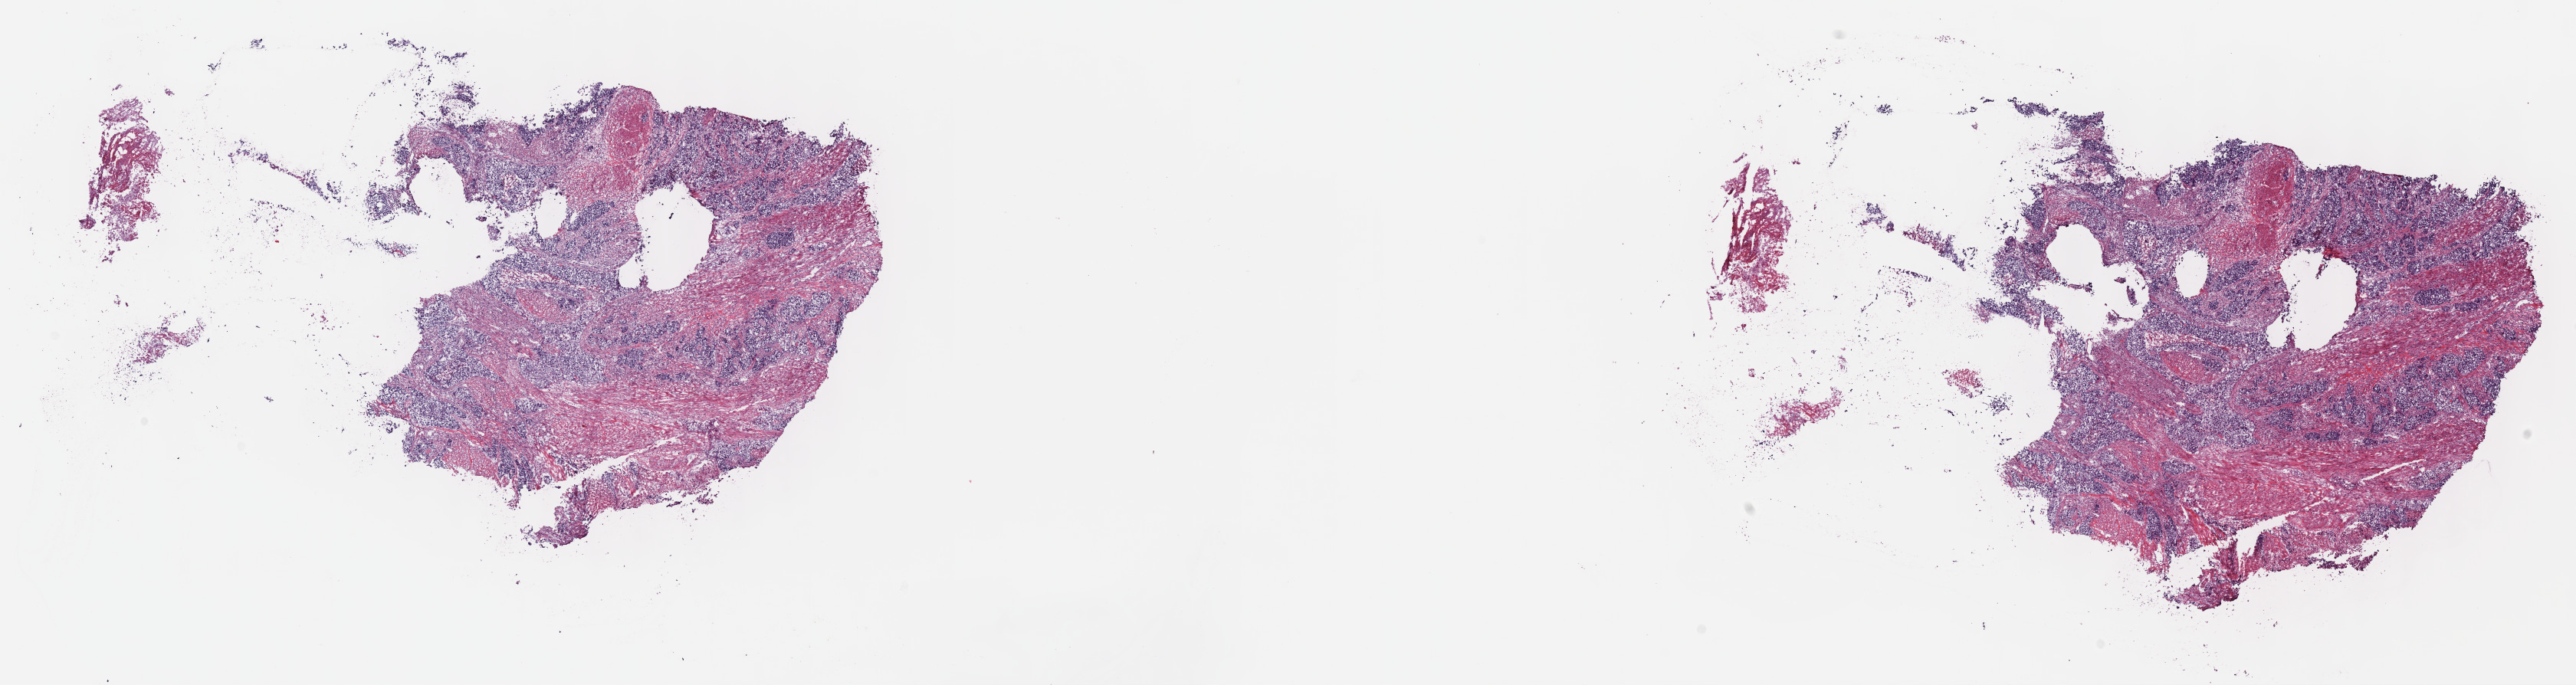
Whole-slide histology image, Hematoxylin and eosin (H&E) stained — shown as a low-resolution overview of the whole scanned area (about 27.2 x 7.2 mm, slide scanned at 40x), frozen section, primary tumour sample from the bladder. Female patient; age at initial diagnosis 81 years. Histologic grade: high grade. Slide review estimates, as recorded: tumour cells 70%, tumour nuclei 70%, normal cells 0%, stromal cells 30%, necrosis 0%. Infiltration values recorded for this section: lymphocyte infiltration 3%, monocyte infiltration 1%, neutrophil infiltration 4%.
Pathologic diagnosis: Transitional cell carcinoma. AJCC pathologic stage: IV (6th edition).